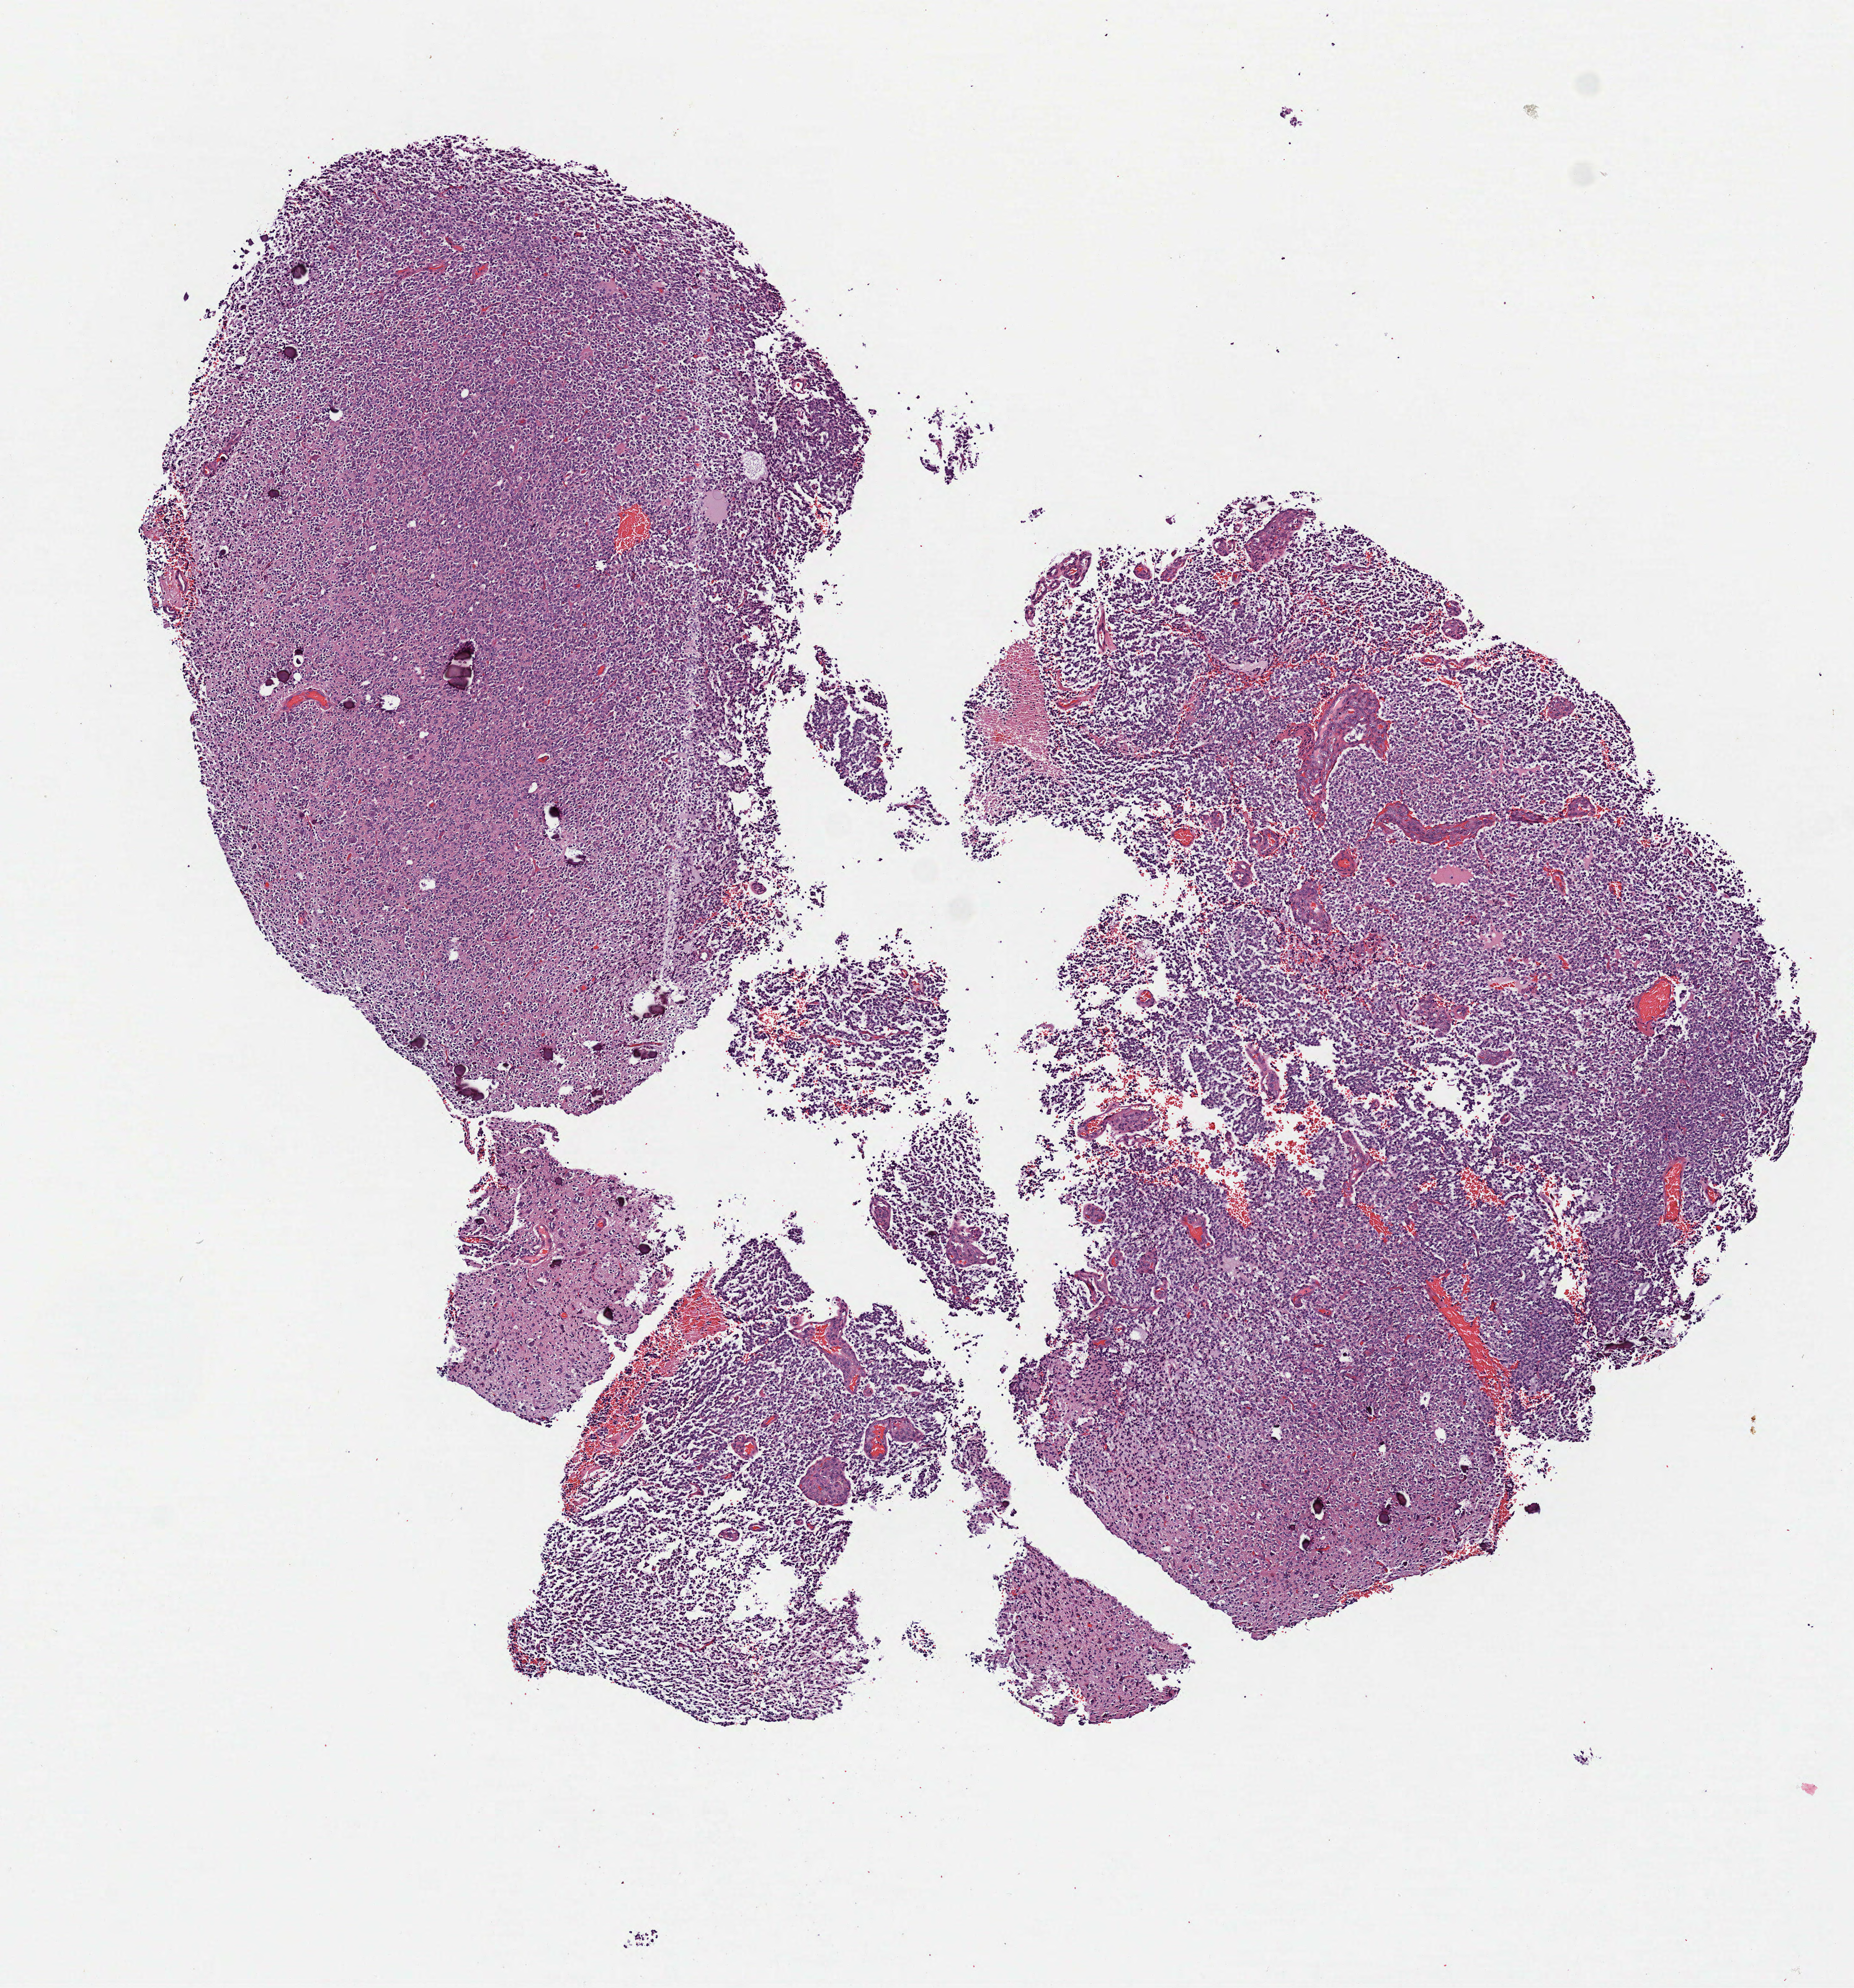
Hematoxylin and eosin (H&E) stained whole-slide image — whole scanned area (about 5.8 x 6.2 mm, acquisition: 40x scan) shown as a low-resolution overview, formalin-fixed paraffin-embedded (FFPE) diagnostic section, primary tumour sample from the brain. Male, age 56 years at initial diagnosis.
Pathologic diagnosis: Oligodendroglioma, anaplastic (cerebrum).